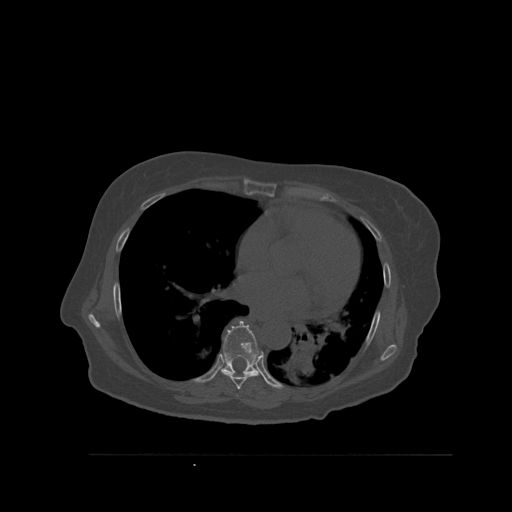
CT including the spine, one axial slice. Bone window (W 1800 / L 400 HU). 1.5 mm slice thickness. 512 × 512 image matrix, field of view 470 × 470 mm. Female patient, age 73 years. From the clinical record (not read from this slice): primary cancer: breast.
Structures marked on this image (semi-automatic segmentation, software-assisted and operator-edited):
- T7 vertebra: bounding box (x1, y1, x2, y2) in pixels: (223, 352, 260, 390)
- T8 vertebra: (221, 321, 262, 376)